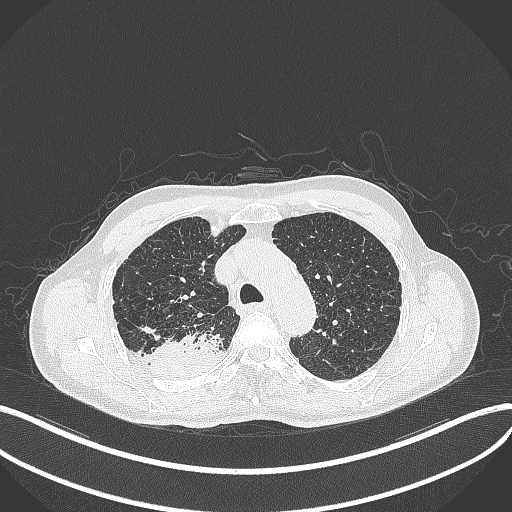
Chest CT, one axial slice; position 331 of 428 along the scan axis; reconstruction kernel B70f; lung window (W 1500 / L -600 HU); 1 mm slice thickness; 512 × 512 image matrix, field of view 400 × 400 mm. Male patient, age 79 years. From the clinical record (not read from this slice): clinical TNM (as recorded): T3 N0 M0.
Annotated regions visible in this slice (rectangle marked by the reading radiologist):
- lung tumour (recorded histology: adenocarcinoma): bounding box <151,330,224,381> (left, top, right, bottom; pixels)